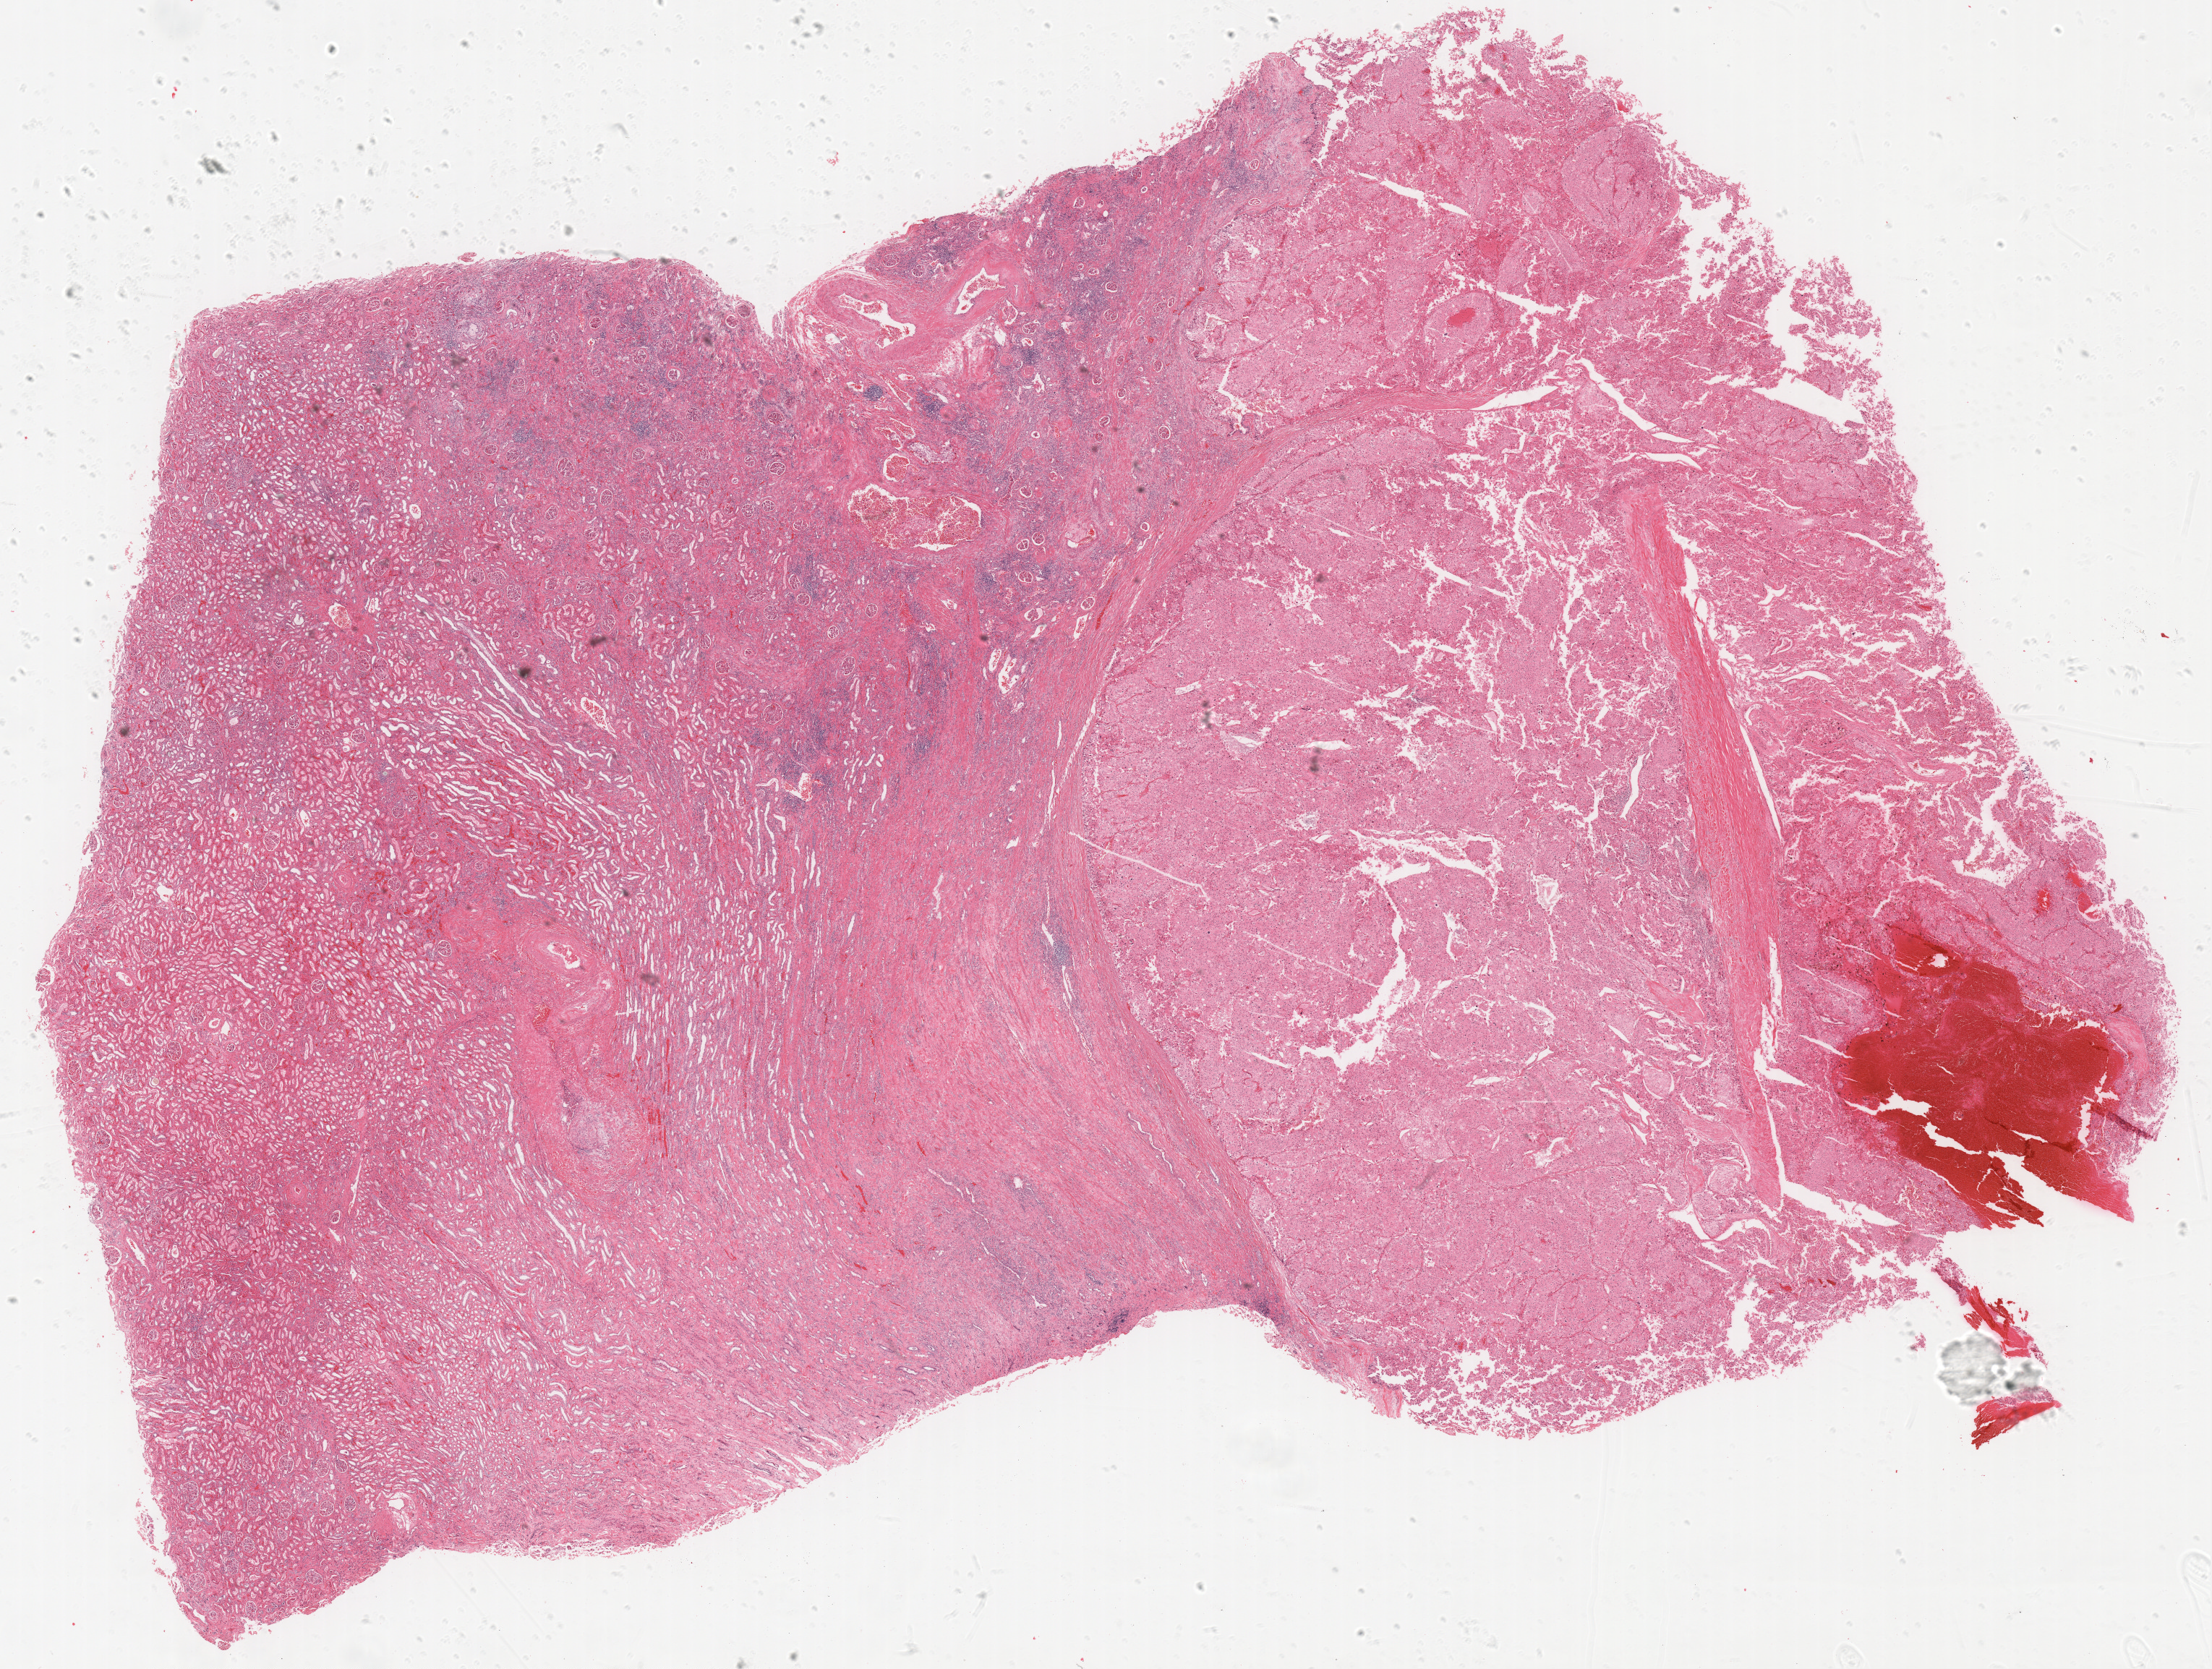
Whole-slide histology image, Hematoxylin and eosin (H&E) stained, whole scanned area (about 24.5 x 18.5 mm) shown as a low-resolution overview. Formalin-fixed paraffin-embedded (FFPE) diagnostic section. Kidney, primary tumour sample. Patient: female, age at initial diagnosis 57 years.
- histologic diagnosis: Renal cell carcinoma, chromophobe type
- AJCC pathologic stage: III (5th edition)
- laterality: right